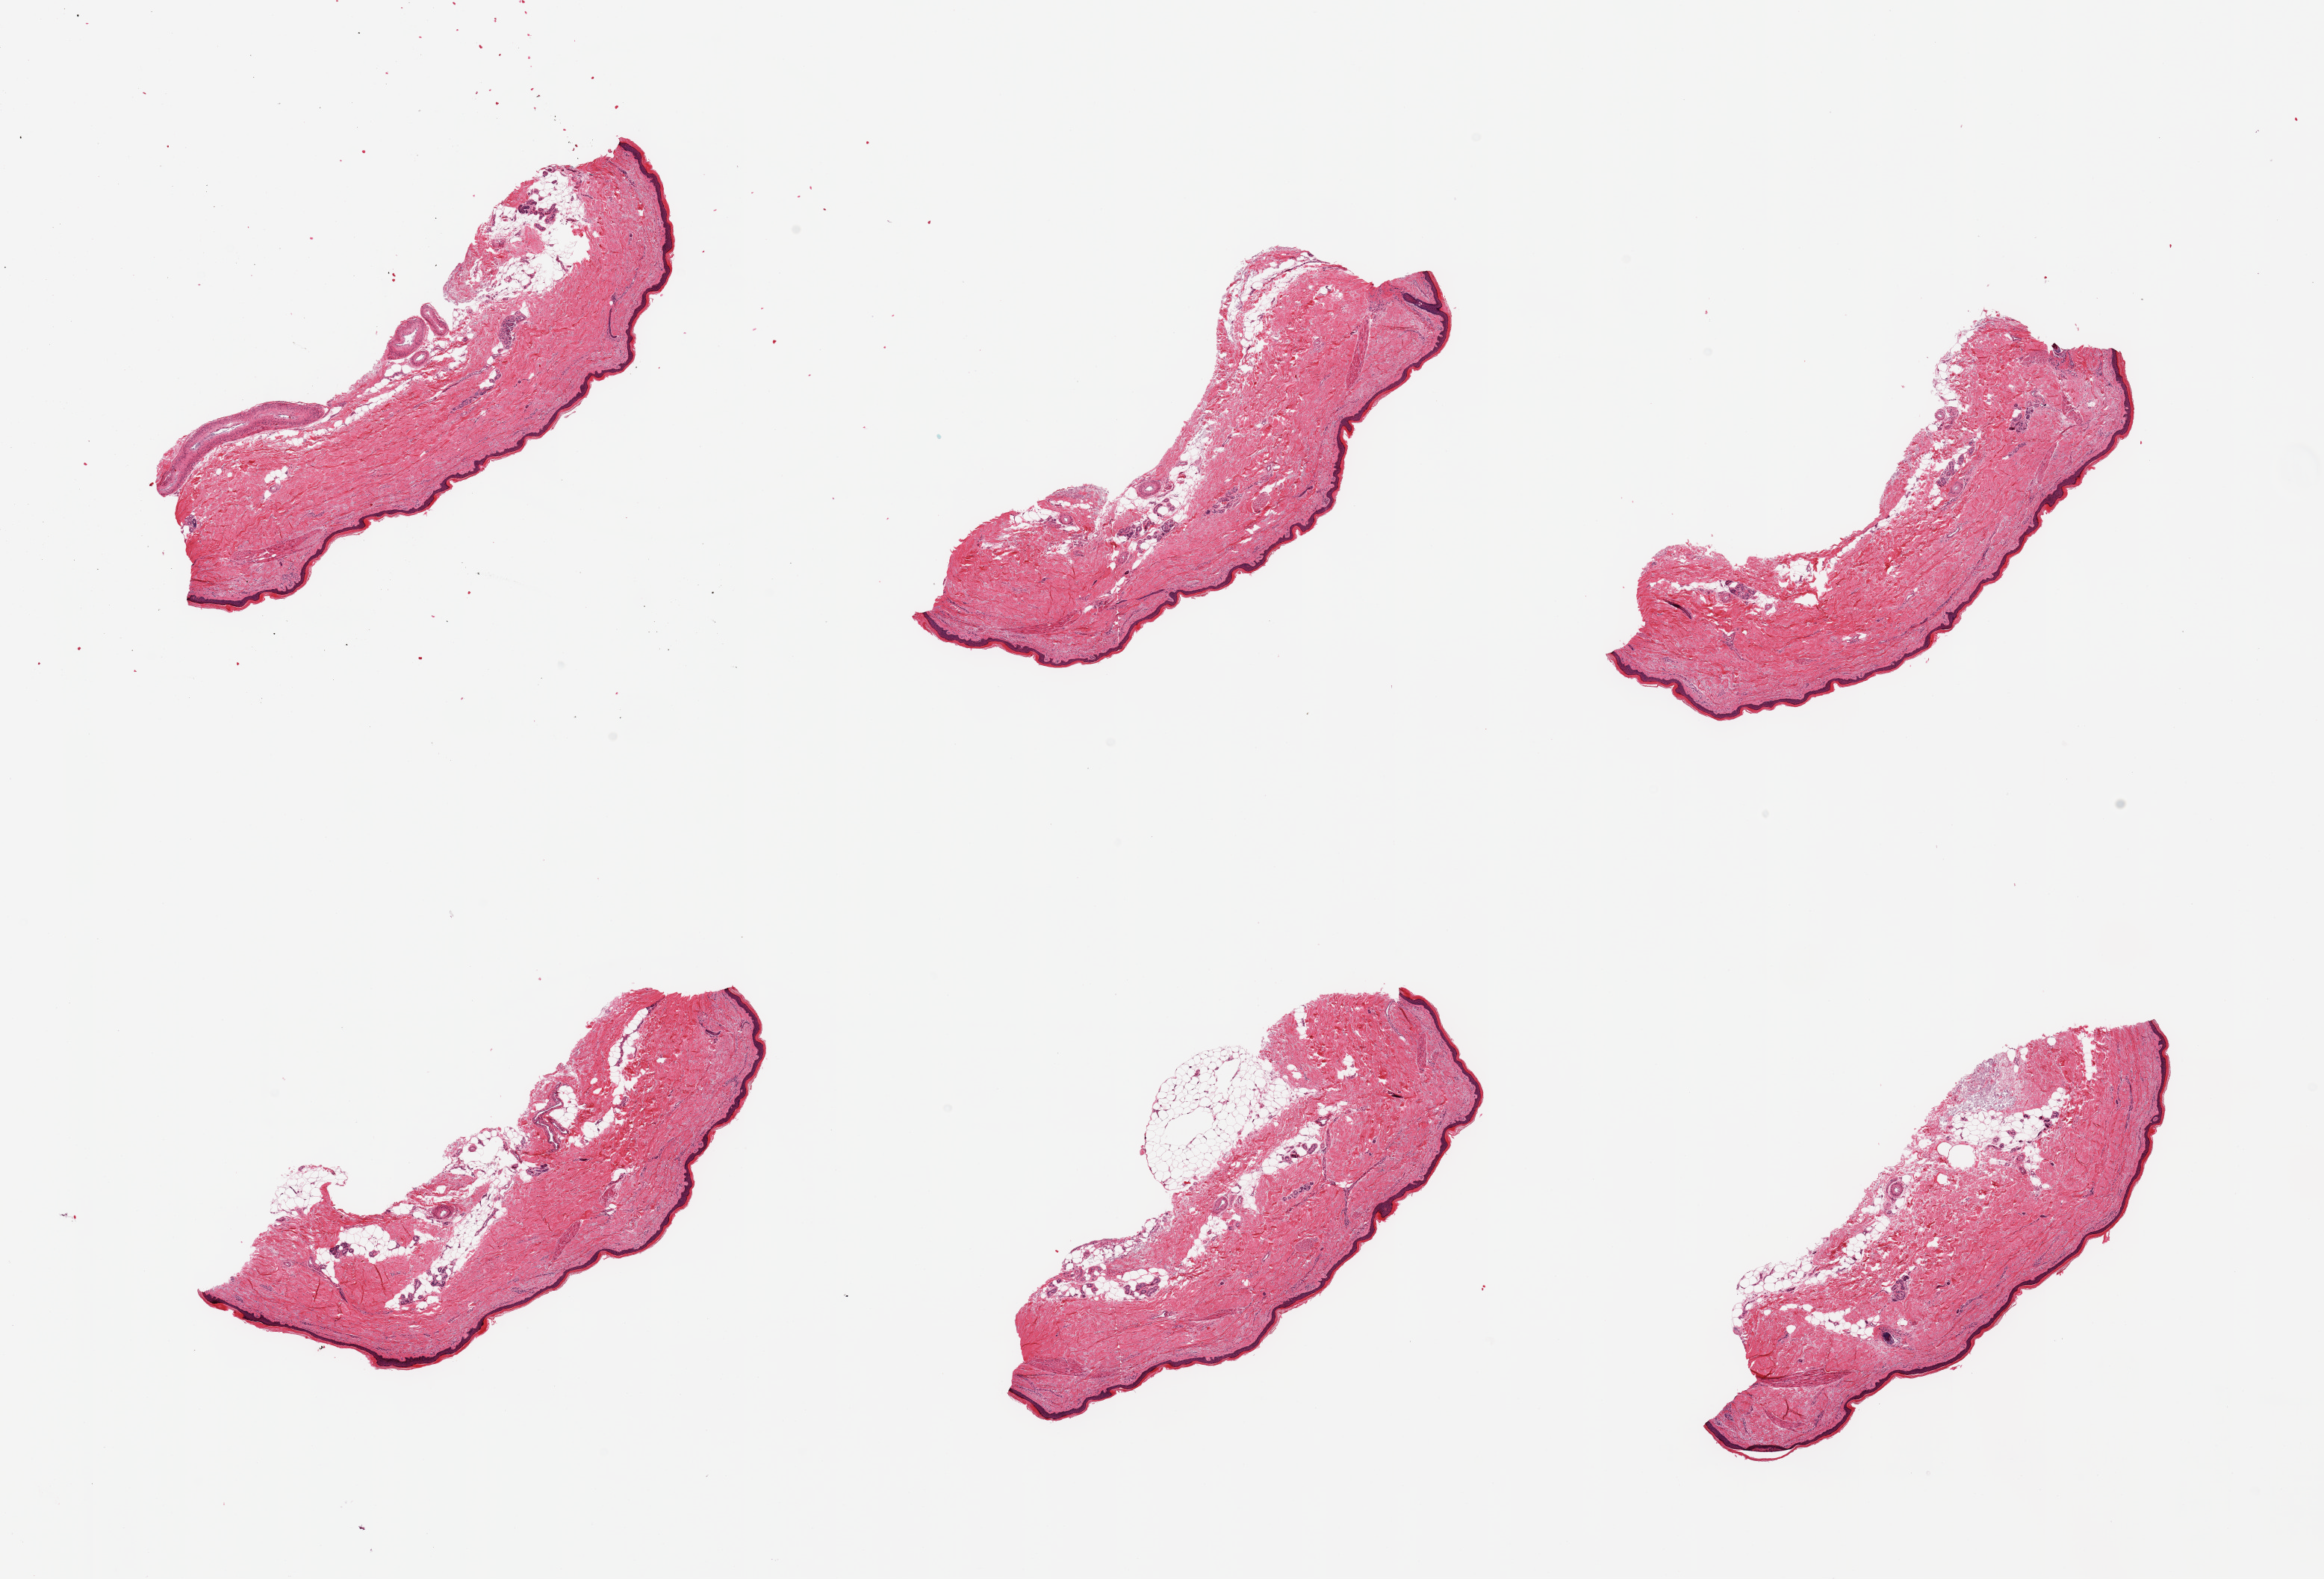
Whole-slide image, haematoxylin and eosin stain, whole scanned area (about 24.6 x 16.7 mm, acquisition: 20x scan) shown as a low-resolution overview; PAXgene-fixed paraffin-embedded (PFPE) section; target tissue: skin of lower leg; donor tissue sample. Female donor.
• review note (as recorded): 6 pieces; generally well trimmed except for deep 1 mm focus of fat in 1 and large blood vessels in another piece; 10-20% dermal fat